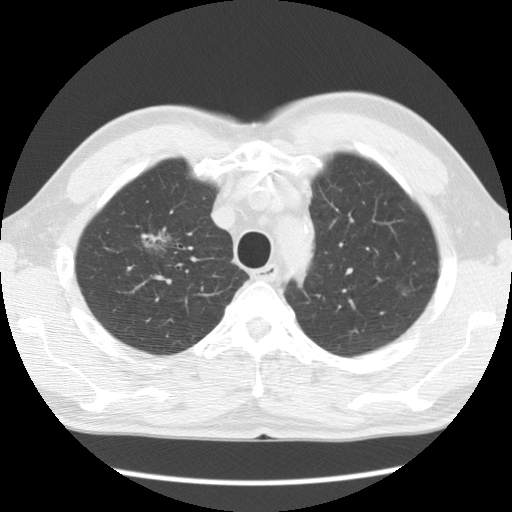
Chest CT (low-dose screening protocol), one axial image. Baseline screening round. Lung window (W 1500 / L -600 HU). 2.5 mm slice thickness. Standard (soft-tissue) reconstruction kernel (STANDARD). Slice 24 of 132 in the series. 512 × 512 image matrix, field of view 340 × 340 mm. Male participant, aged 64 years at enrolment. Former smoker at enrolment.
- Lesion marked by an expert reader, bounding box <96,193,180,274> (left, top, right, bottom; pixels).
- The screening reader recorded 2 non-calcified nodules or masses ≥4 mm on this exam; which of them this box marks is not recorded.
- Official screen result: positive, change unspecified: nodule(s) >= 4 mm or enlarging nodule(s), mass(es), or other non-specific abnormalities suspicious for lung cancer.
- Participant outcome: lung cancer diagnosed 750 days after this screen — adenocarcinoma, NOS, right upper lobe, well differentiated (G1), stage IB (AJCC 6th edition), 45 mm at pathology.